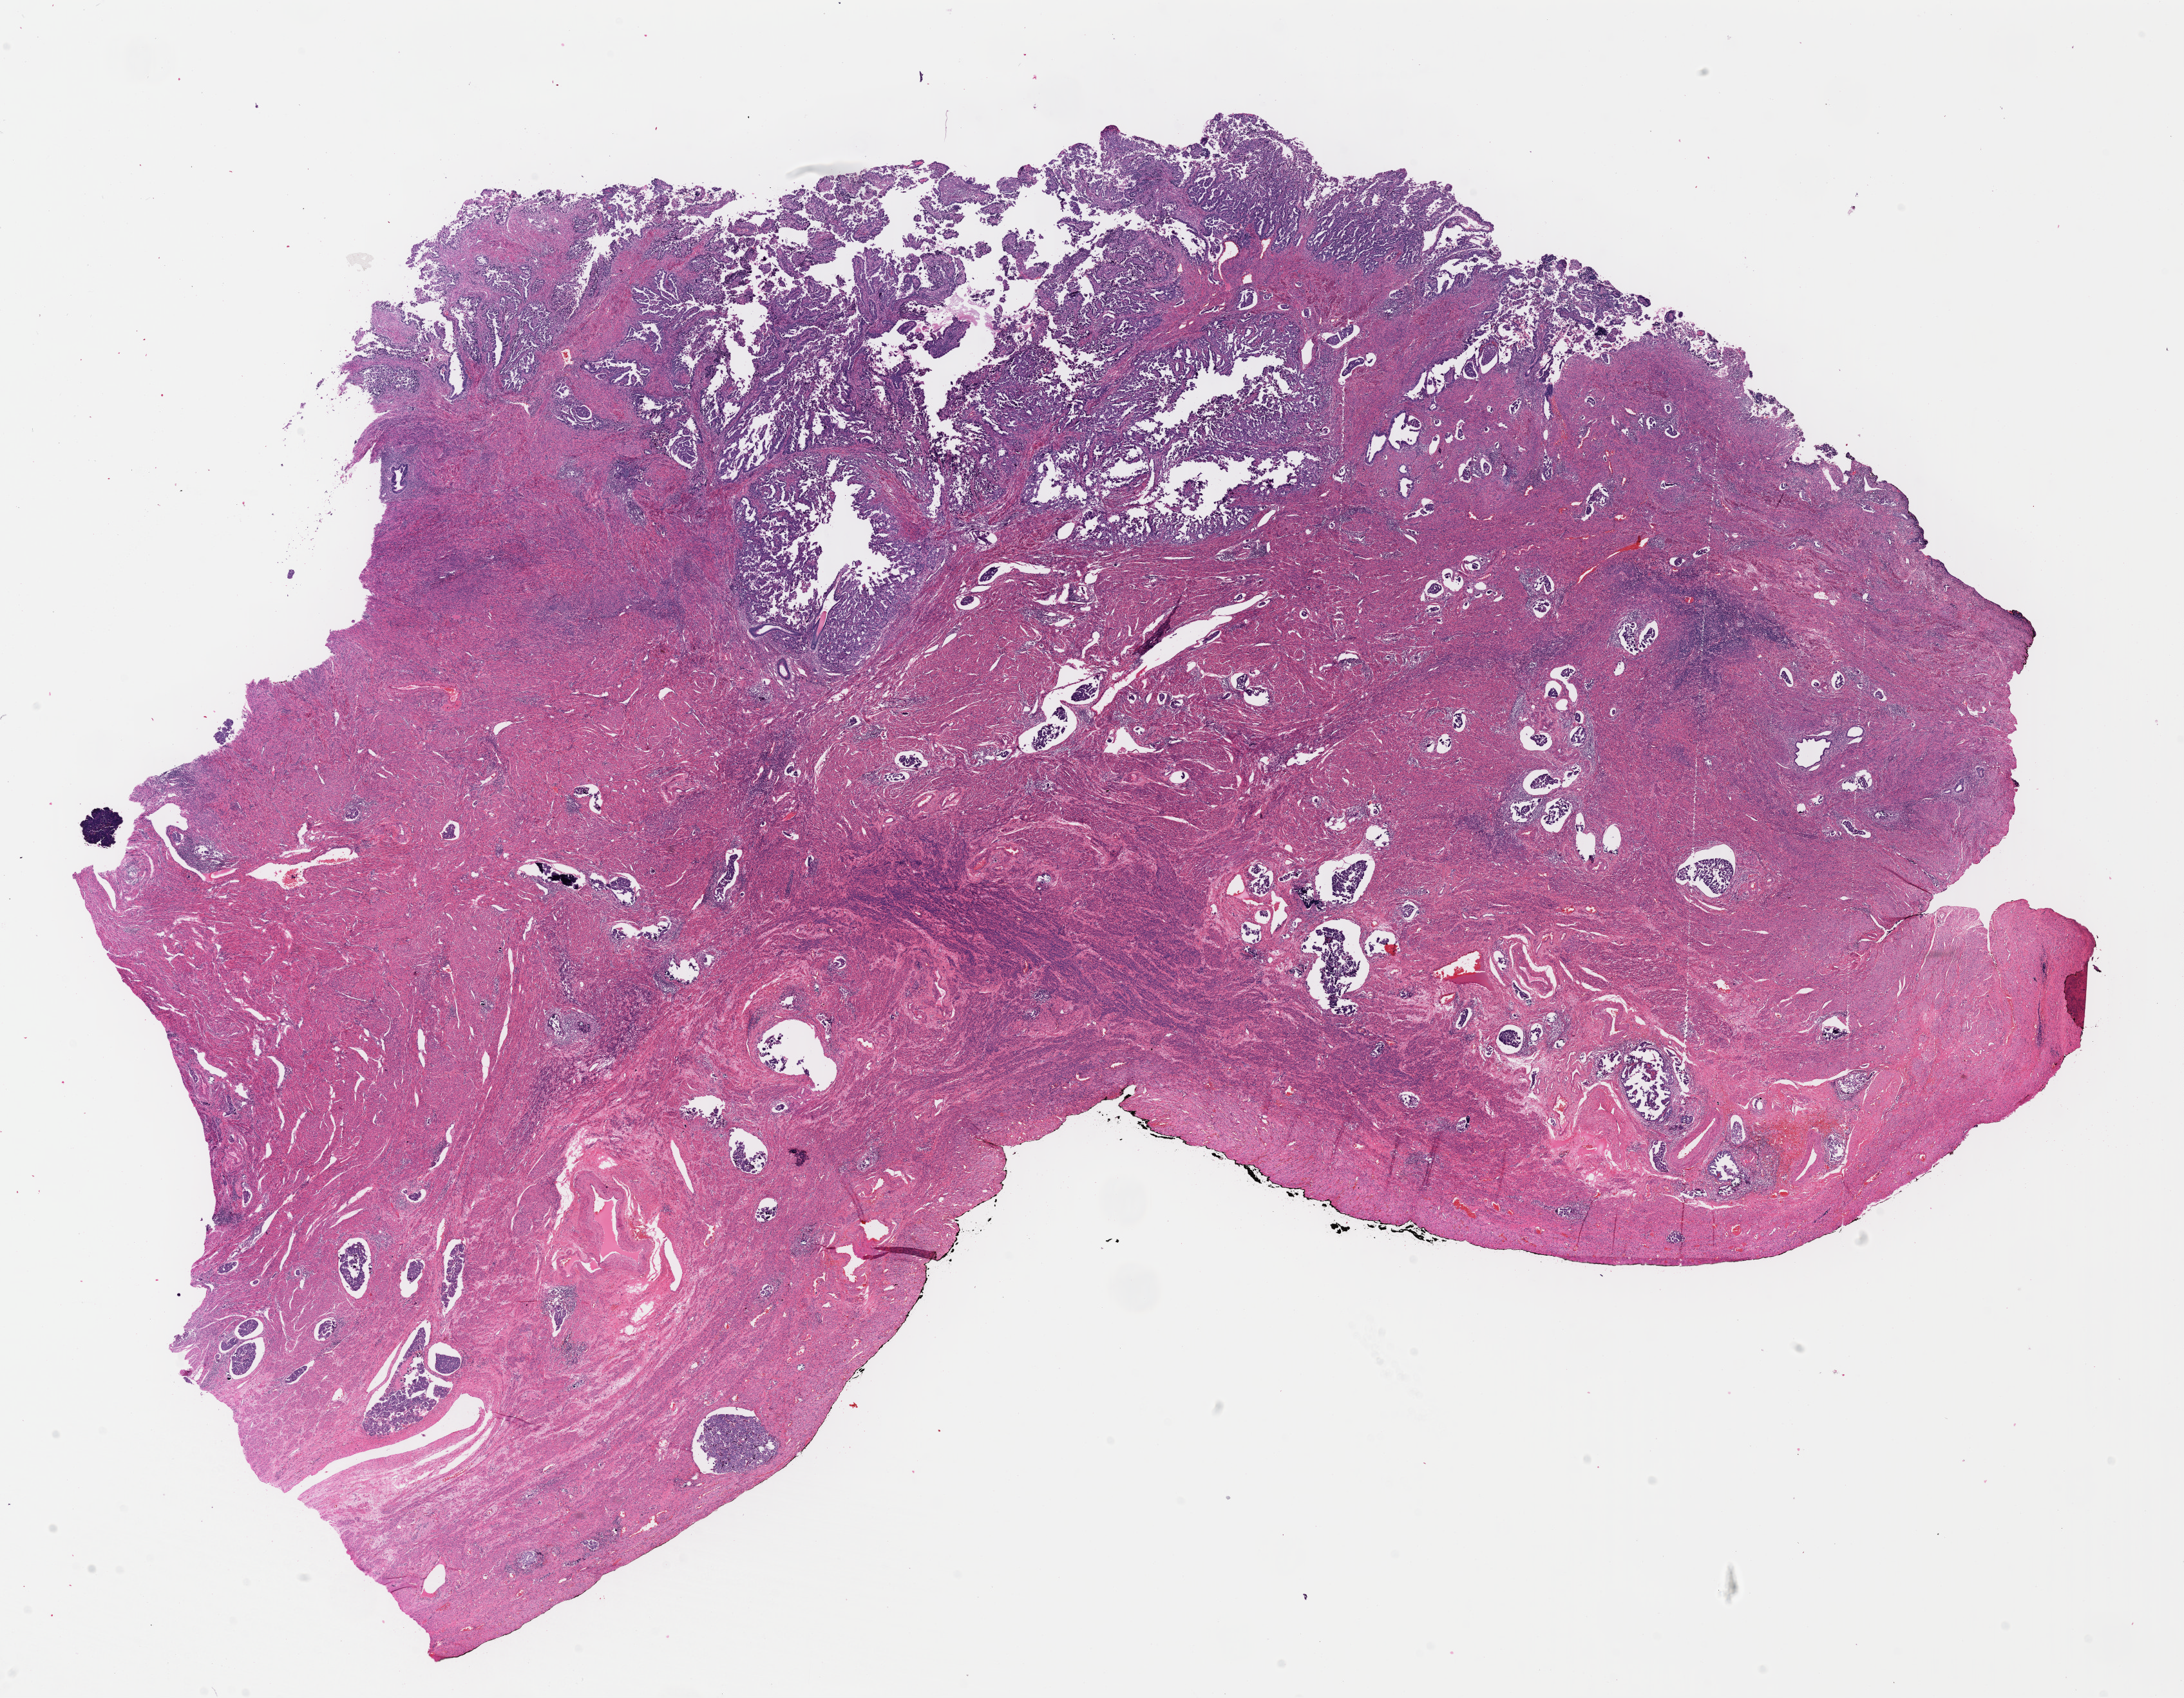
Digitized Hematoxylin and eosin (H&E) stained tissue section (whole slide), shown as a low-resolution overview of the whole scanned area (about 26.7 x 20.7 mm, slide scanned at 40x). Formalin-fixed paraffin-embedded (FFPE) diagnostic section. Primary tumour sample from the uterus. Patient: female, age at initial diagnosis 70 years. Histologic grade: G3 (poorly differentiated).
* pathologic diagnosis: Serous cystadenocarcinoma, NOS (endometrium)
* FIGO stage: IIIC1